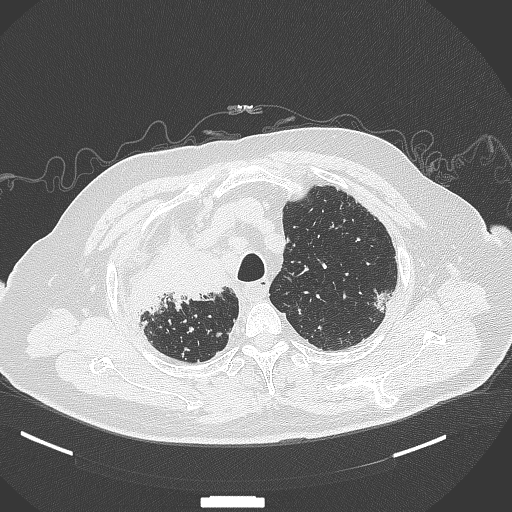
Chest CT, one axial slice. 120 kVp. Lung window (W 1500 / L -600 HU). 1 mm slice thickness. 512 × 512 image matrix, field of view 400 × 400 mm. Patient: male, 69 years. Case-level facts recorded for this patient, not image findings: clinical TNM (as recorded): T4 N3 M1.
Annotated regions visible in this slice (rectangle marked by the reading radiologist):
- lung tumour (recorded histology: adenocarcinoma): bounding box [x1, y1, x2, y2] px = [134, 243, 227, 320]